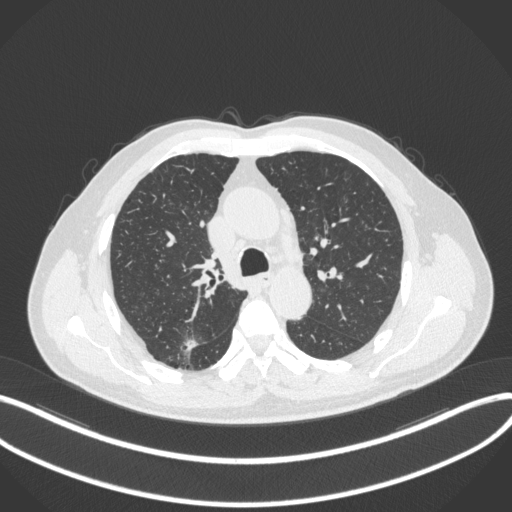
Chest CT, one axial slice; position 252 of 366 along the scan axis; reconstruction kernel B31f; 120 kVp; lung window (W 1500 / L -600 HU); 1 mm slice thickness; 512 × 512 image matrix, field of view 400 × 400 mm. Male patient, age 69 years. Case-level facts recorded for this patient, not image findings: clinical TNM (as recorded): T1b N0 M0.
Annotated regions visible in this slice (rectangle marked by the reading radiologist):
- lung tumour (recorded histology: adenocarcinoma): bounding box <180,334,198,357> (left, top, right, bottom; pixels)